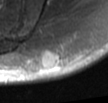
MRI of an extremity soft-tissue mass, one axial slice; position 12 of 42 along the scan axis; T2-weighted fat-saturated; MR volume resampled by the dataset authors to the PET/CT grid (not the native acquisition matrix); 108 × 103 image matrix, field of view 105 × 101 mm. Male patient. Case-level facts recorded for this patient, not image findings: histological type: leiomyosarcoma; grade: intermediate; site of the primary tumour: left pelvis.
Outlined on this slice (expert contour drawn on MRI and transferred to this co-registered scan by the dataset authors):
- gross tumour volume (mass): box from (x=41, y=49) to (x=63, y=70) px